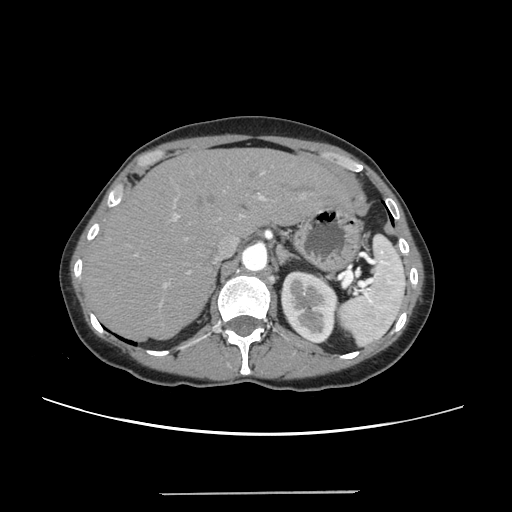
Contrast-enhanced abdominal CT, one axial slice. Slice 174 of 240 in the series (ordered by position). 120 kVp. Intravenous contrast given. Soft-tissue window (W 400 / L 40 HU). 1.25 mm slice thickness. 512 × 512 image matrix. Female patient, age 60 years. Case-level facts recorded for this patient, not image findings: diagnosis: colorectal cancer liver metastases, imaged before liver resection; multiple liver metastases: no; largest metastasis: 1.5 cm; disease in both lobes: no.
Structures marked on this image (expert manual segmentation):
- liver: bounding box (x1, y1, x2, y2) in pixels: (86, 150, 348, 339)
- planned liver remnant (the part of the liver to remain after resection): (86, 150, 349, 339)
- portal vein (with intrahepatic branches): (135, 171, 305, 287)